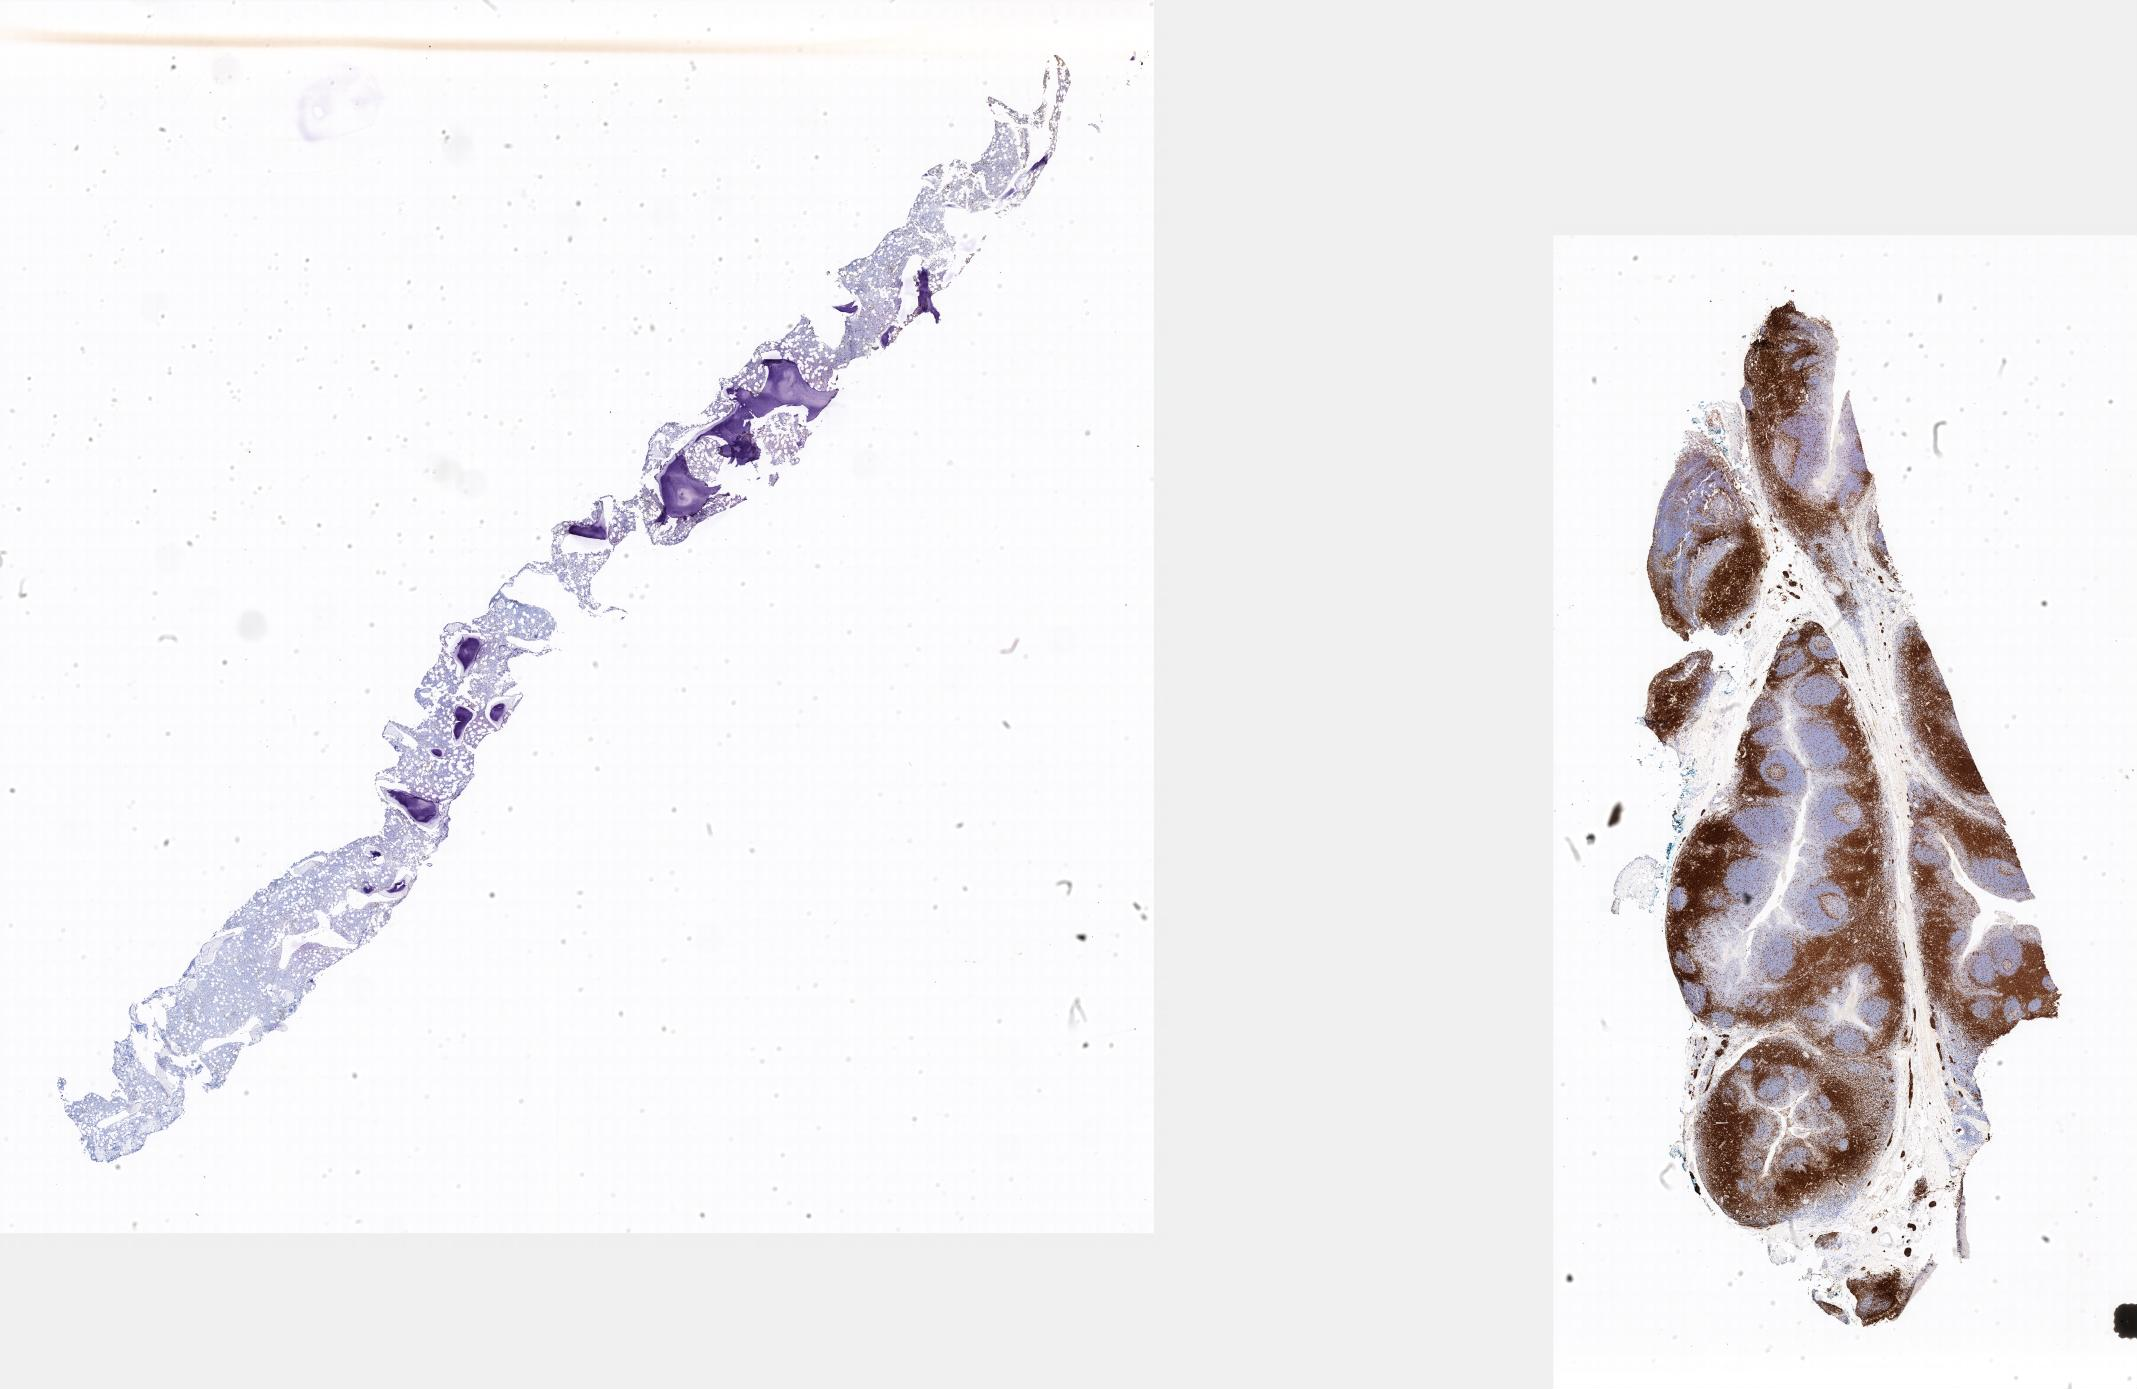
Immunohistochemistry (IHC) whole-slide image stained for CD3 — shown as a low-resolution overview of the whole scanned area; tumor tissue; site: bone marrow. Male patient, 20 years old.
* histologic diagnosis: Diffuse large B-cell lymphoma, NOS